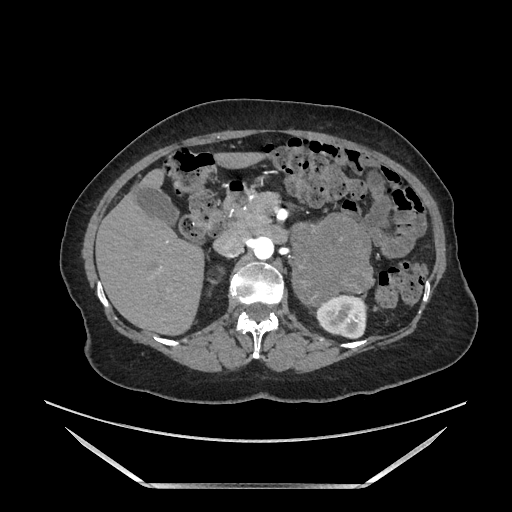
Contrast-enhanced abdominal CT, one axial slice. Position 99 of 205 along the scan axis. Soft-tissue window (W 400 / L 40 HU). 512 × 512 image matrix, field of view 440 × 440 mm. Female patient. From the clinical record (not read from this slice): diagnosis: adrenocortical carcinoma; tumour side: left adrenal.
Structures marked on this image (semi-automatically segmented with operator editing):
- mass: bounding box <292,215,371,303> (left, top, right, bottom; pixels)